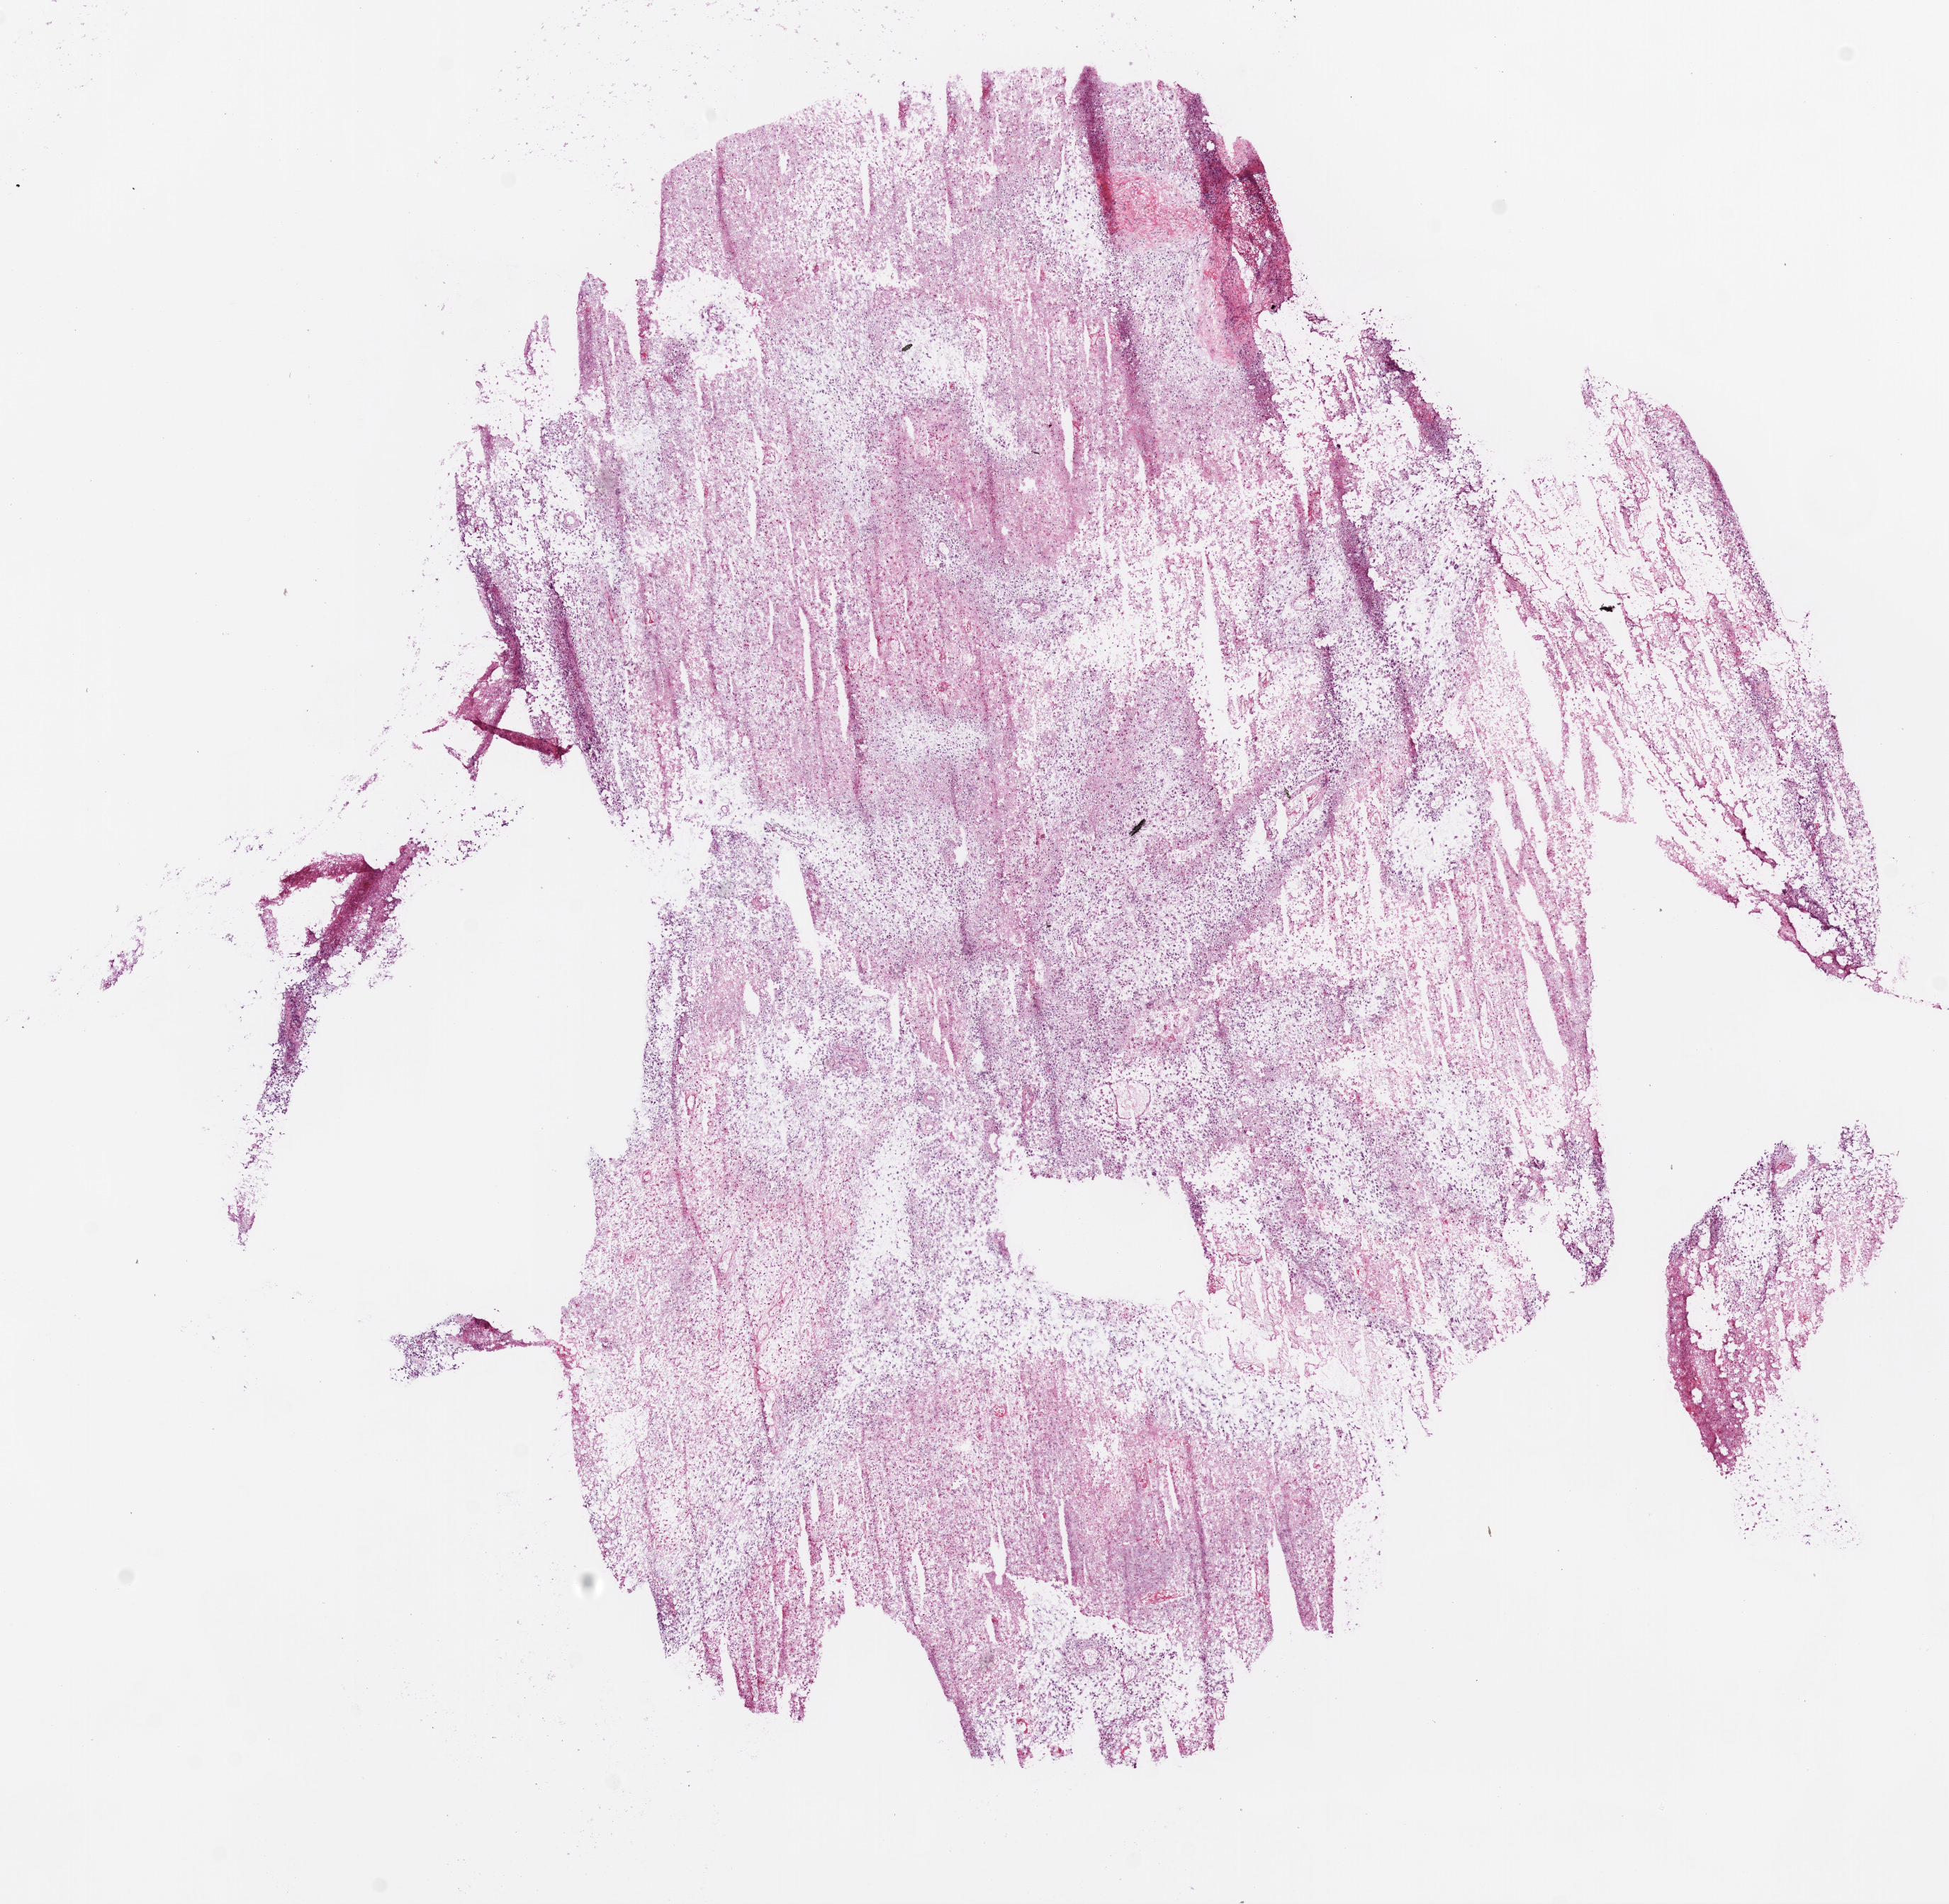
Digitized Hematoxylin and eosin (H&E) stained tissue section (whole slide) — low-resolution overview of the scanned area, about 11.0 x 10.8 mm (acquisition: 20x scan), frozen section from the bottom of the tissue portion, sample: primary tumour, brain. Patient: male, age at initial diagnosis 56 years. Pathologist review of this section (percent, as recorded): tumour cells 70%, tumour nuclei 85%, normal cells 0%, stromal cells 0%, necrosis 30%.
Histologic diagnosis: Glioblastoma.